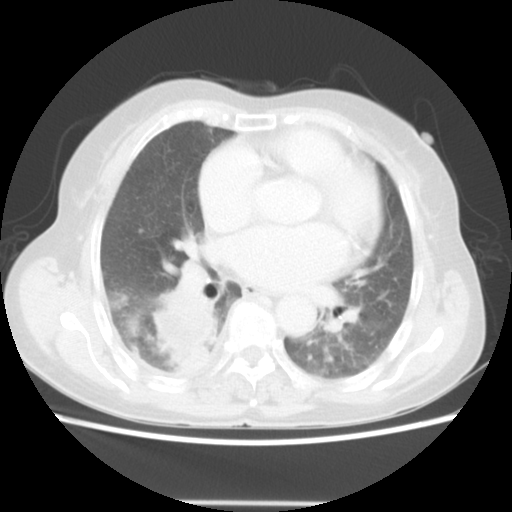
Chest CT, one axial slice; position 25 of 52 along the scan axis; 140 kVp; lung window (W 1500 / L -600 HU); 5 mm slice thickness; 512 × 512 image matrix. Female patient, age 67 years. From the clinical record (not read from this slice): clinical TNM (as recorded): T3 N1 M1.
Outlined on this slice (bounding box drawn by a radiologist):
- lung tumour (recorded histology: adenocarcinoma): bounding box (x1, y1, x2, y2) in pixels: (144, 278, 225, 376)